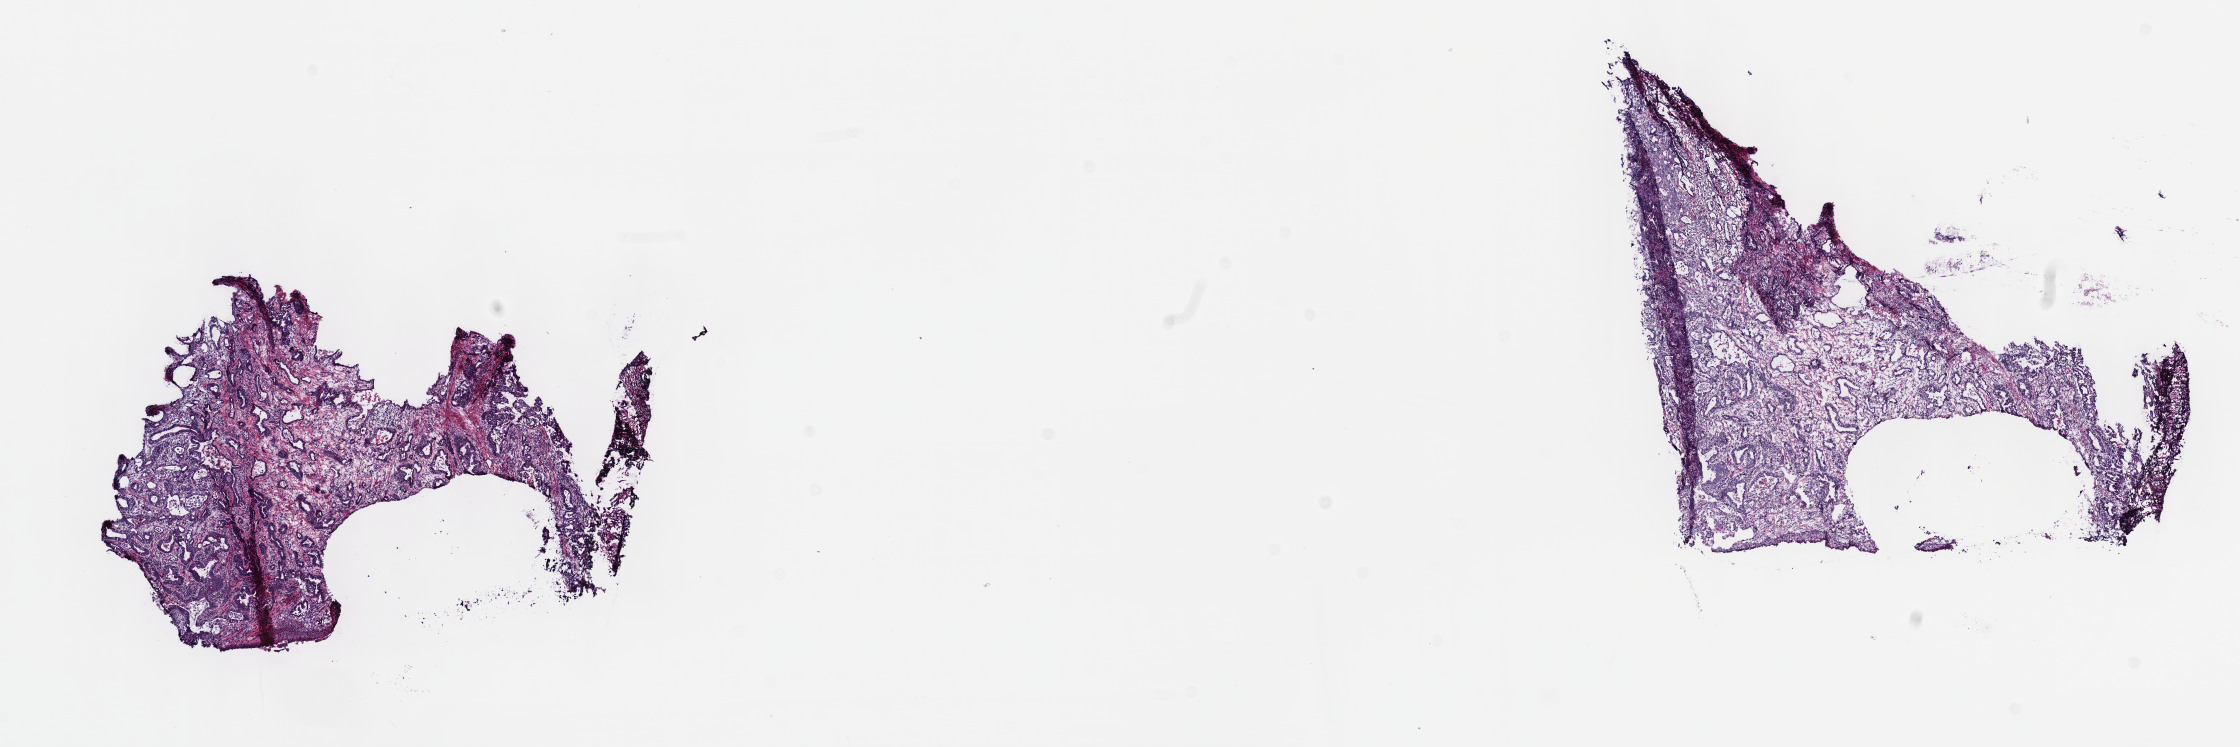
Whole-slide histology image, H&E — low-resolution overview of the scanned area, about 18.1 x 6.0 mm. Frozen section. Esophagus, primary tumour sample. Patient: male, age at initial diagnosis 47 years. Histologic grade: G3 (poorly differentiated). Pathologist review of this section (percent, as recorded): tumour cells 80%, tumour nuclei 80%, normal cells 0%, stromal cells 20%, necrosis 0%. Inflammatory infiltration, as recorded: lymphocyte infiltration 40%, monocyte infiltration 20%, neutrophil infiltration 20%.
• pathologic diagnosis: Adenocarcinoma, NOS (lower third of esophagus)
• AJCC pathologic stage: IIIB